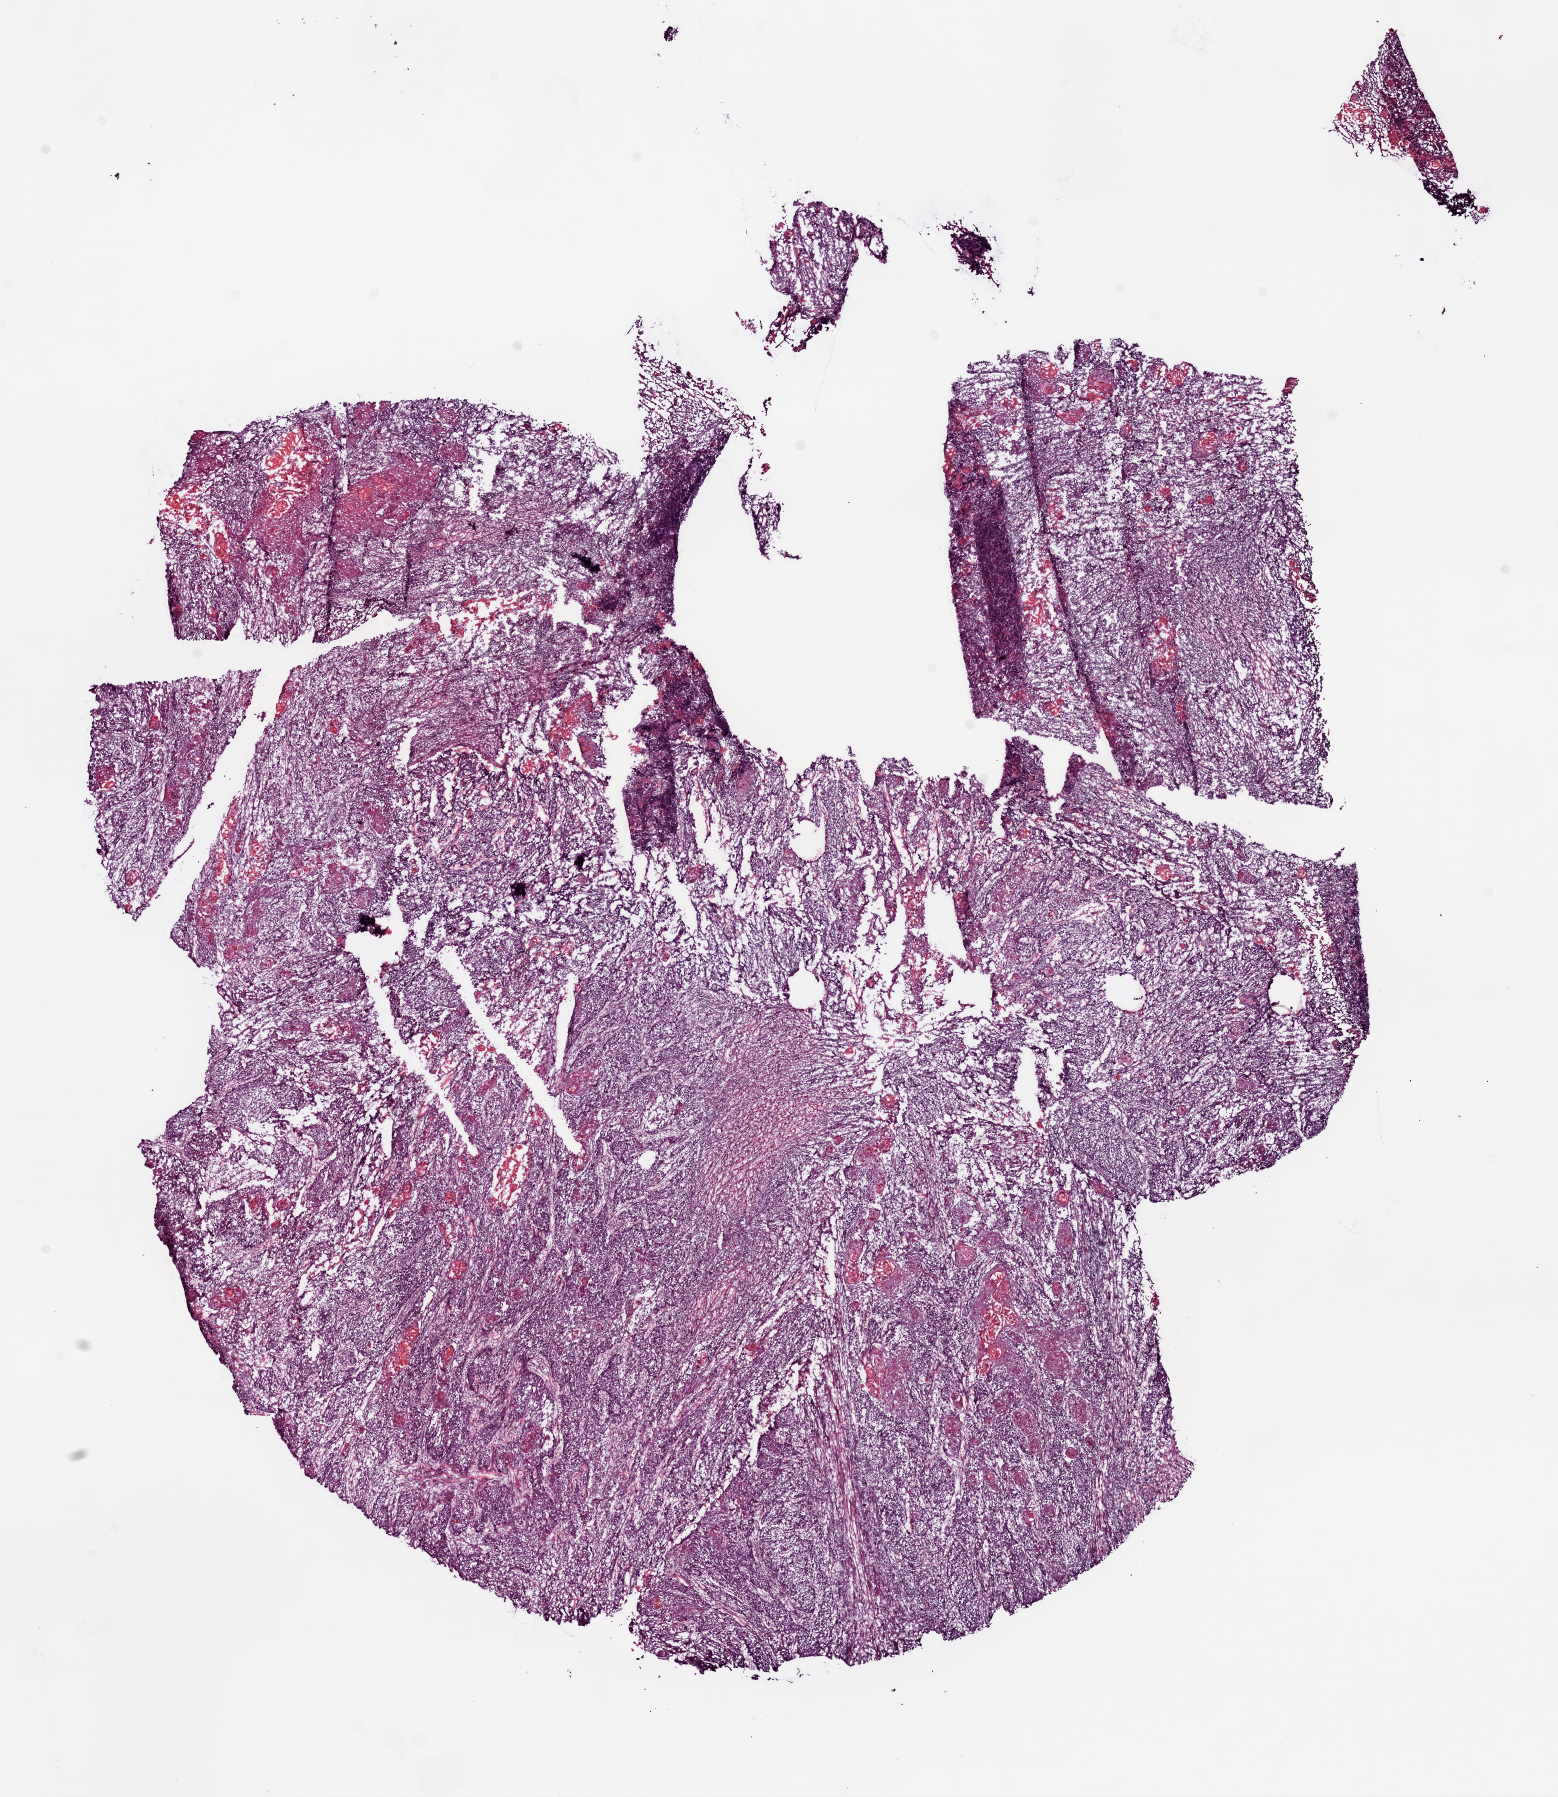
Digitized H&E tissue section (whole slide), low-resolution overview of the scanned area, about 12.6 x 14.5 mm (from a 20x scan). Frozen section. Primary tumour sample from the head and neck. Patient: male, age at initial diagnosis 78 years. Histologic grade: G2 (moderately differentiated). Pathologist review of this section (percent, as recorded): tumour cells 85%, tumour nuclei 50%, normal cells 0%, stromal cells 15%, necrosis 0%.
Lymph nodes positive (case pathology): 0 of 51 examined. AJCC pathologic stage: IVA (7th edition). Diagnosis: Squamous cell carcinoma, NOS (floor of mouth, NOS).